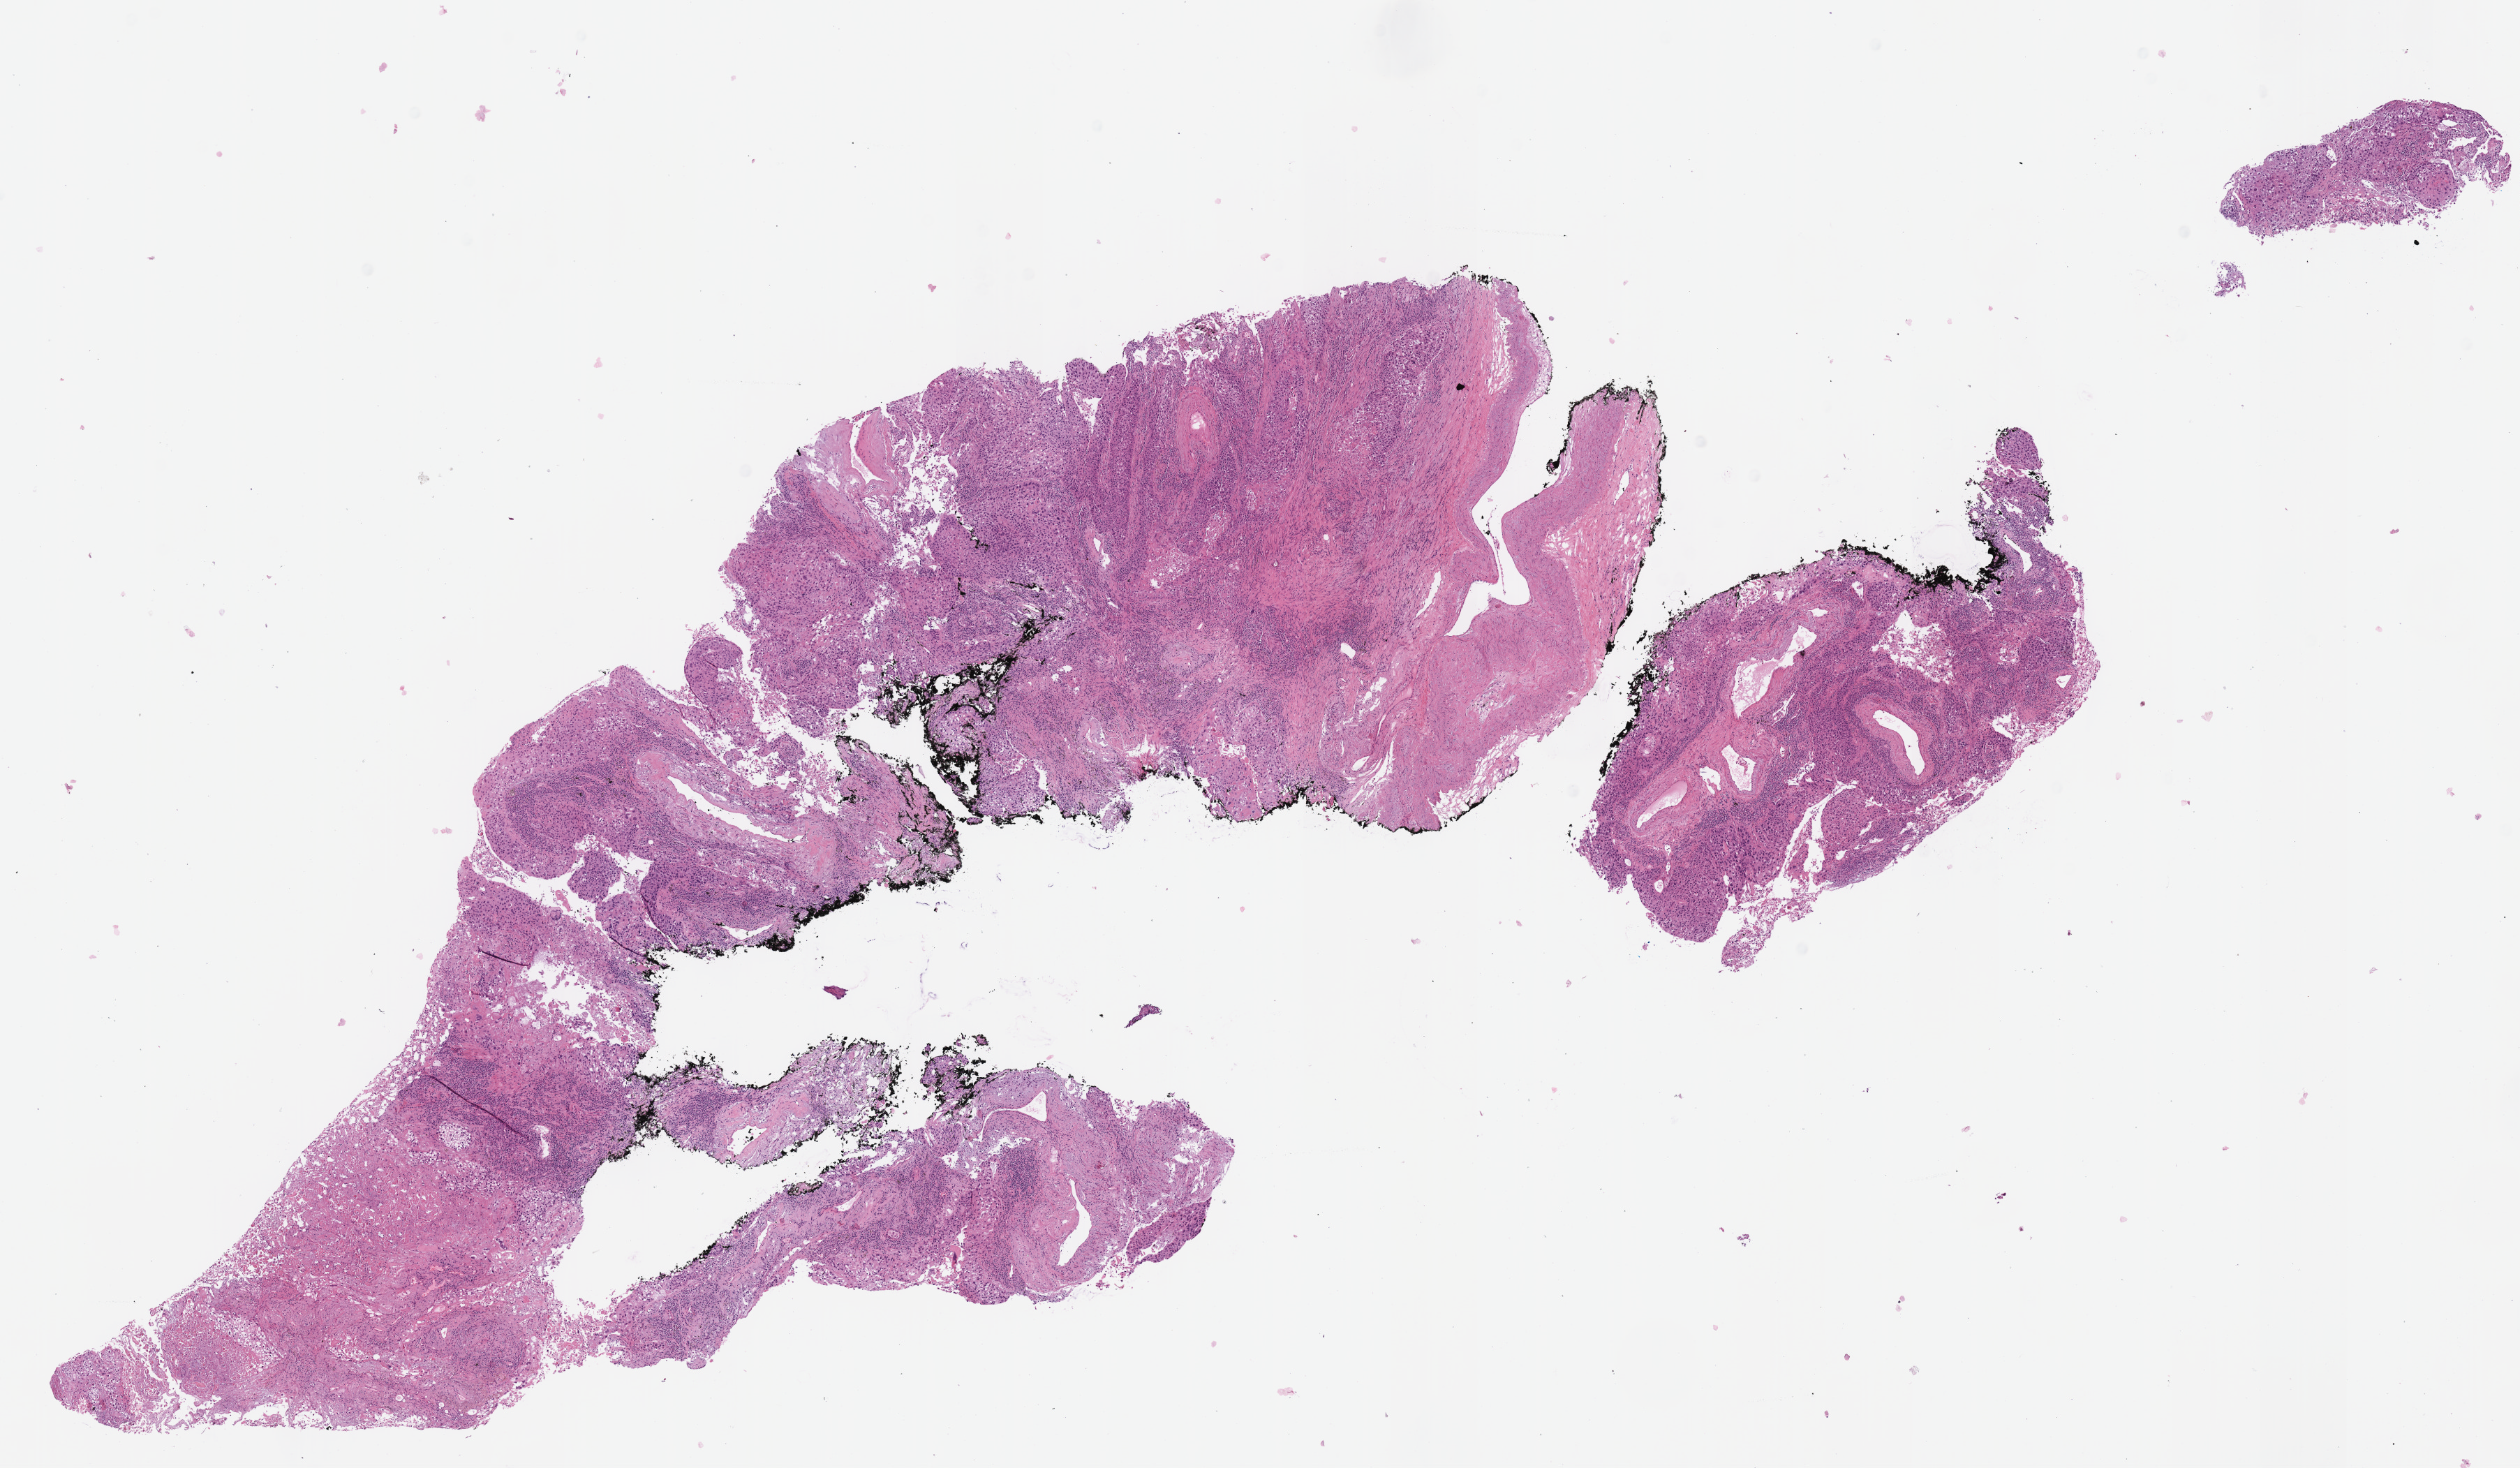
H&E-stained whole-slide image, whole scanned area (about 14.2 x 8.3 mm) shown as a low-resolution overview. Formalin-fixed paraffin-embedded (FFPE) diagnostic section. Lung, primary tumour sample. Patient: female, age at initial diagnosis 73 years.
Laterality: right. AJCC pathologic stage: IA. Pathologic diagnosis: Squamous cell carcinoma, NOS (upper lobe, lung).